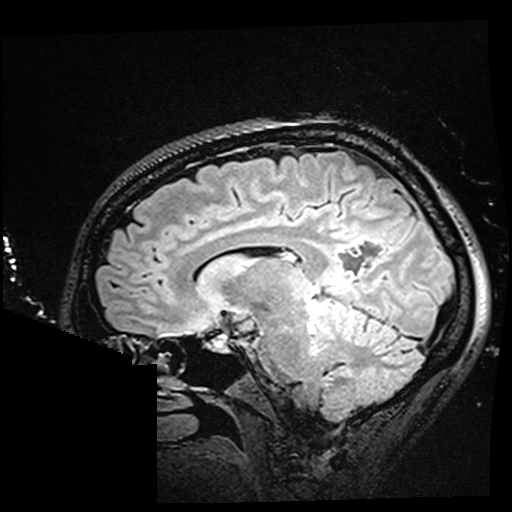
Brain MRI from a brain-tumour surgery series, one sagittal slice; position 101 of 176 along the scan axis; T2 FLAIR; 1 mm slice thickness; 512 × 512 image matrix, field of view 250 × 250 mm. From the clinical record (not read from this slice): histopathology: Oligodendroglioma; WHO grade: 2; IDH mutation: yes; tumour location: Right Parietal.
Outlined on this slice (expert manual segmentation):
- residual tumour: bounding box (x1, y1, x2, y2) in pixels: (323, 273, 353, 294)